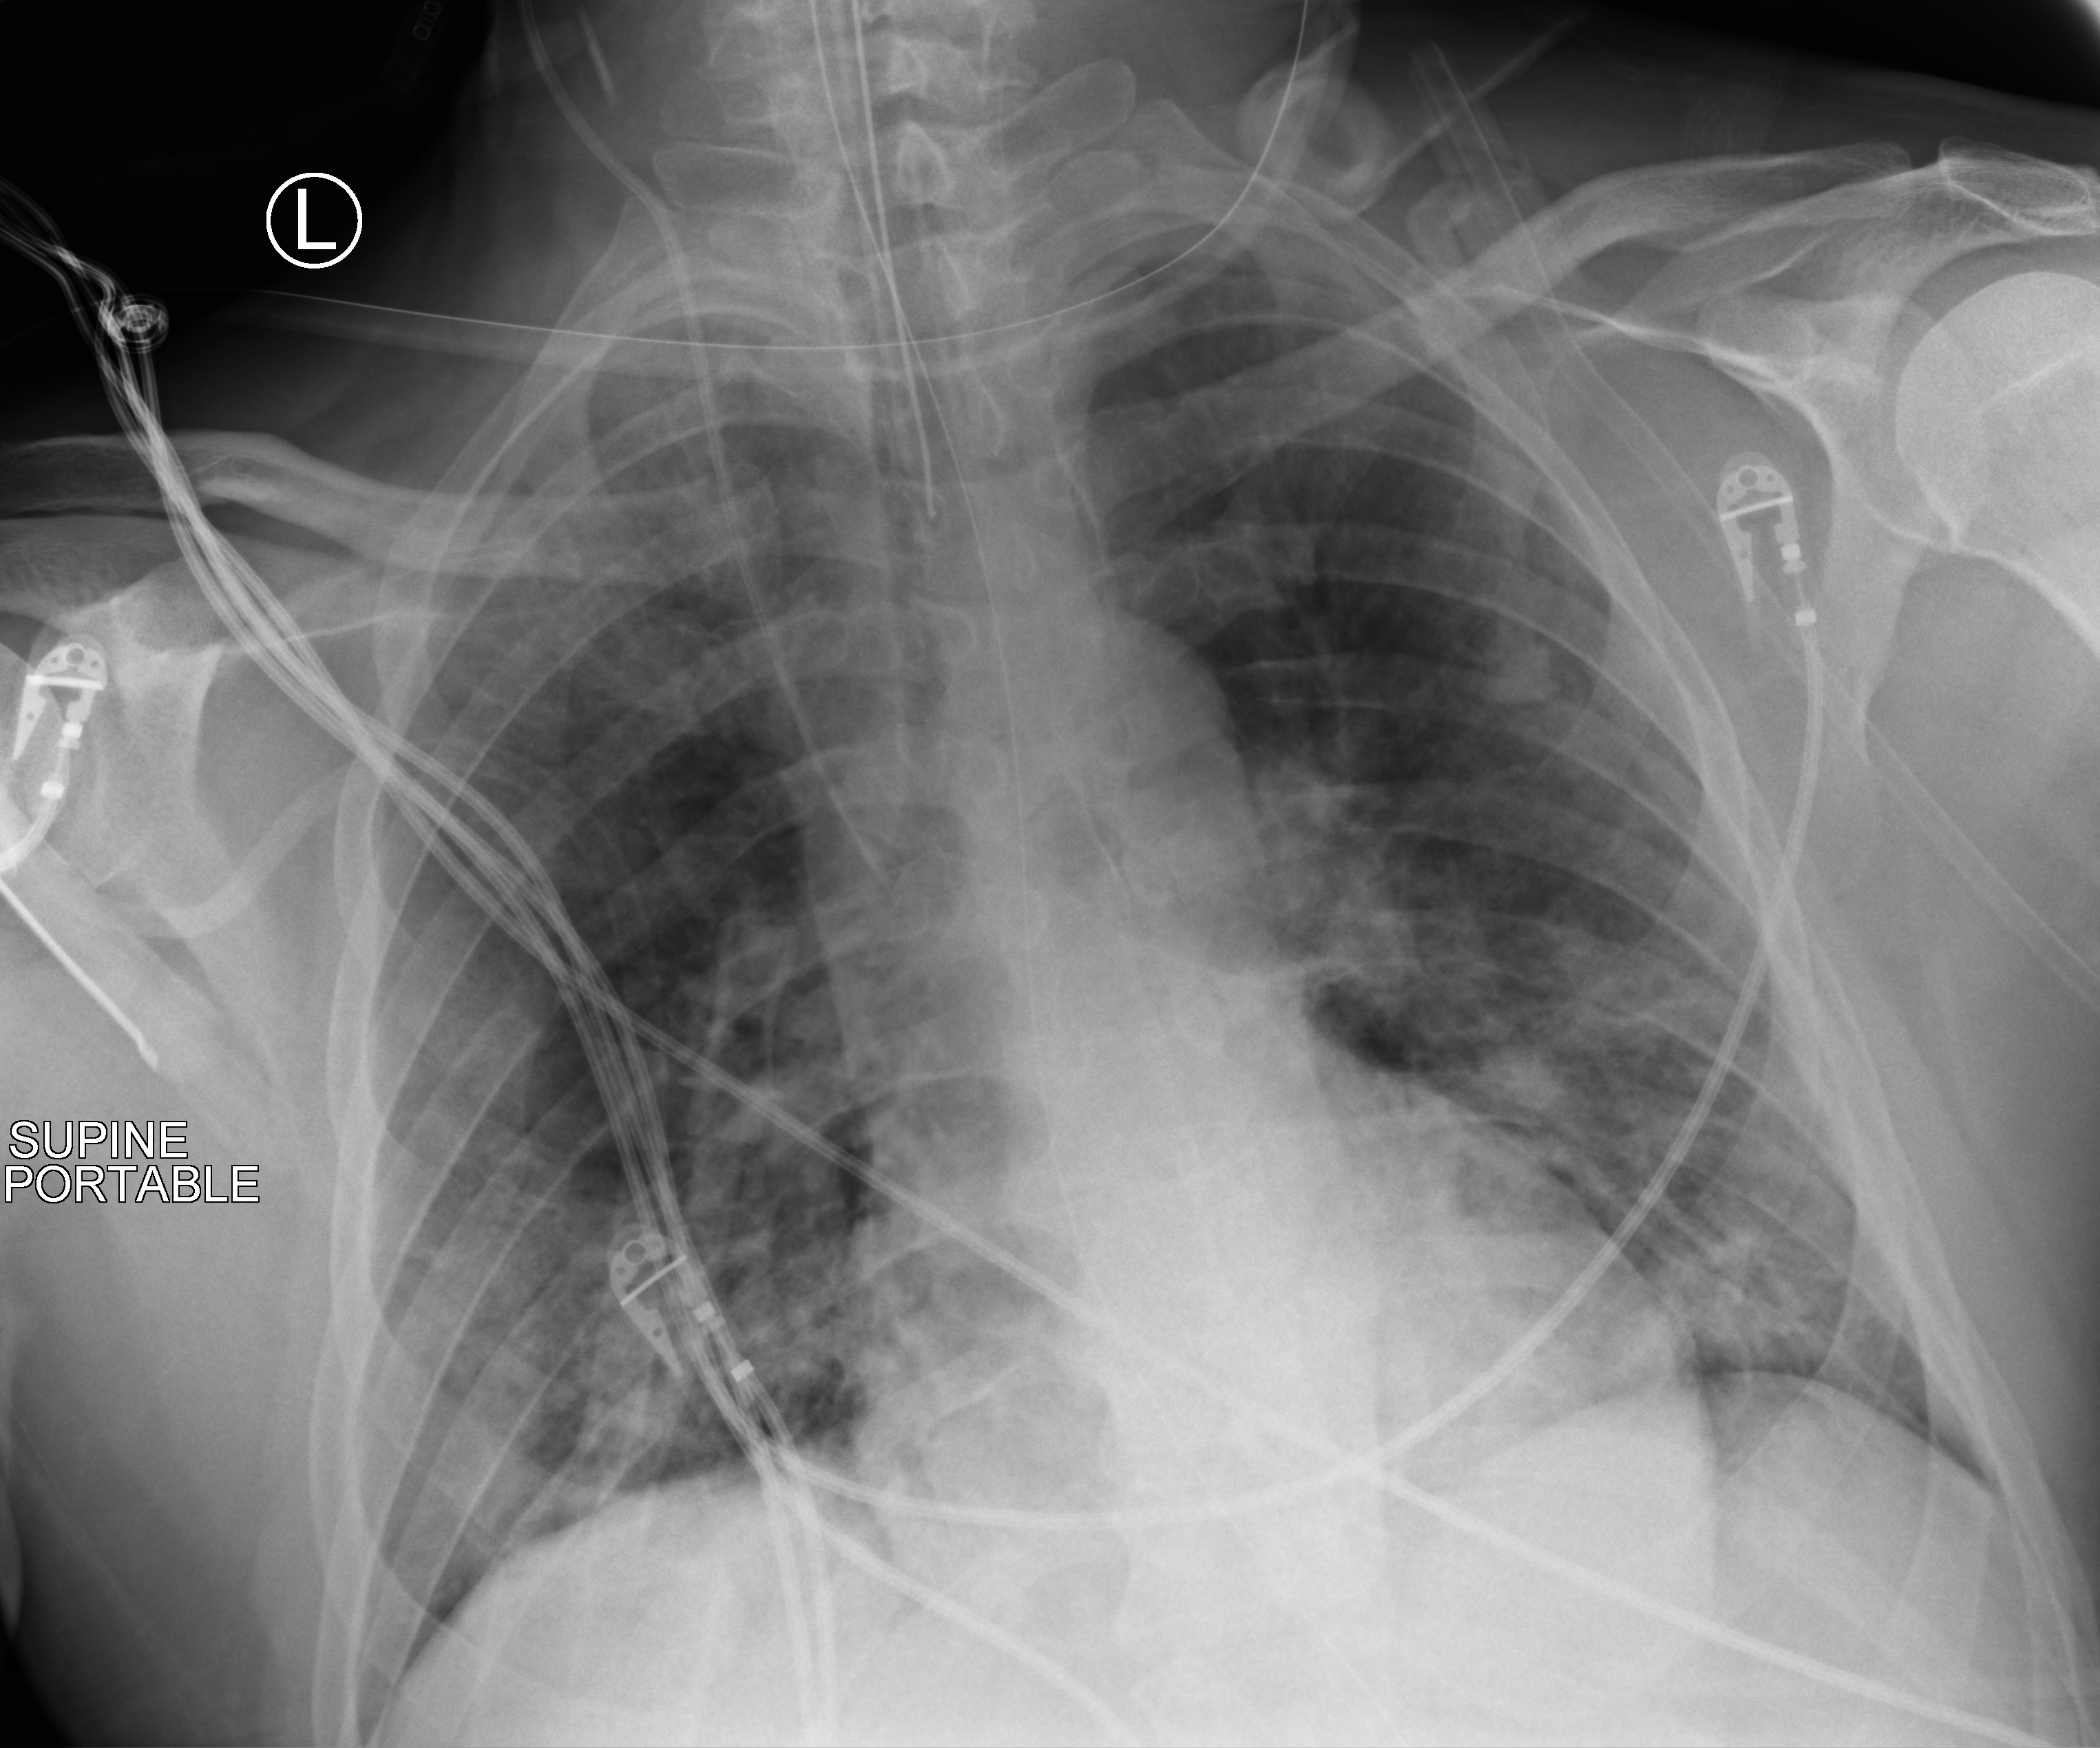
Portable chest radiograph, anteroposterior (AP) projection. Male patient hospitalised with COVID-19, age 18–59 years.
Hospital-stay facts (about this admission, not read from this image; timing relative to this image not recorded): mechanically ventilated during this hospital stay: yes.